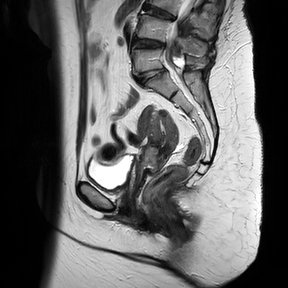
Pelvic MRI for cervical cancer, one sagittal slice. Slice 20 of 37 in the series (ordered by position). T2-weighted. 1.5 T. TE 100 ms, TR 4174.1 ms. 4 mm slice thickness. 288 × 288 image matrix, field of view 300 × 300 mm. Patient: female, 65 years.
Annotated regions visible in this slice (outlined manually by an expert reader):
- uterus and cervix: bounding box (x1, y1, x2, y2) in pixels: (139, 108, 179, 179)